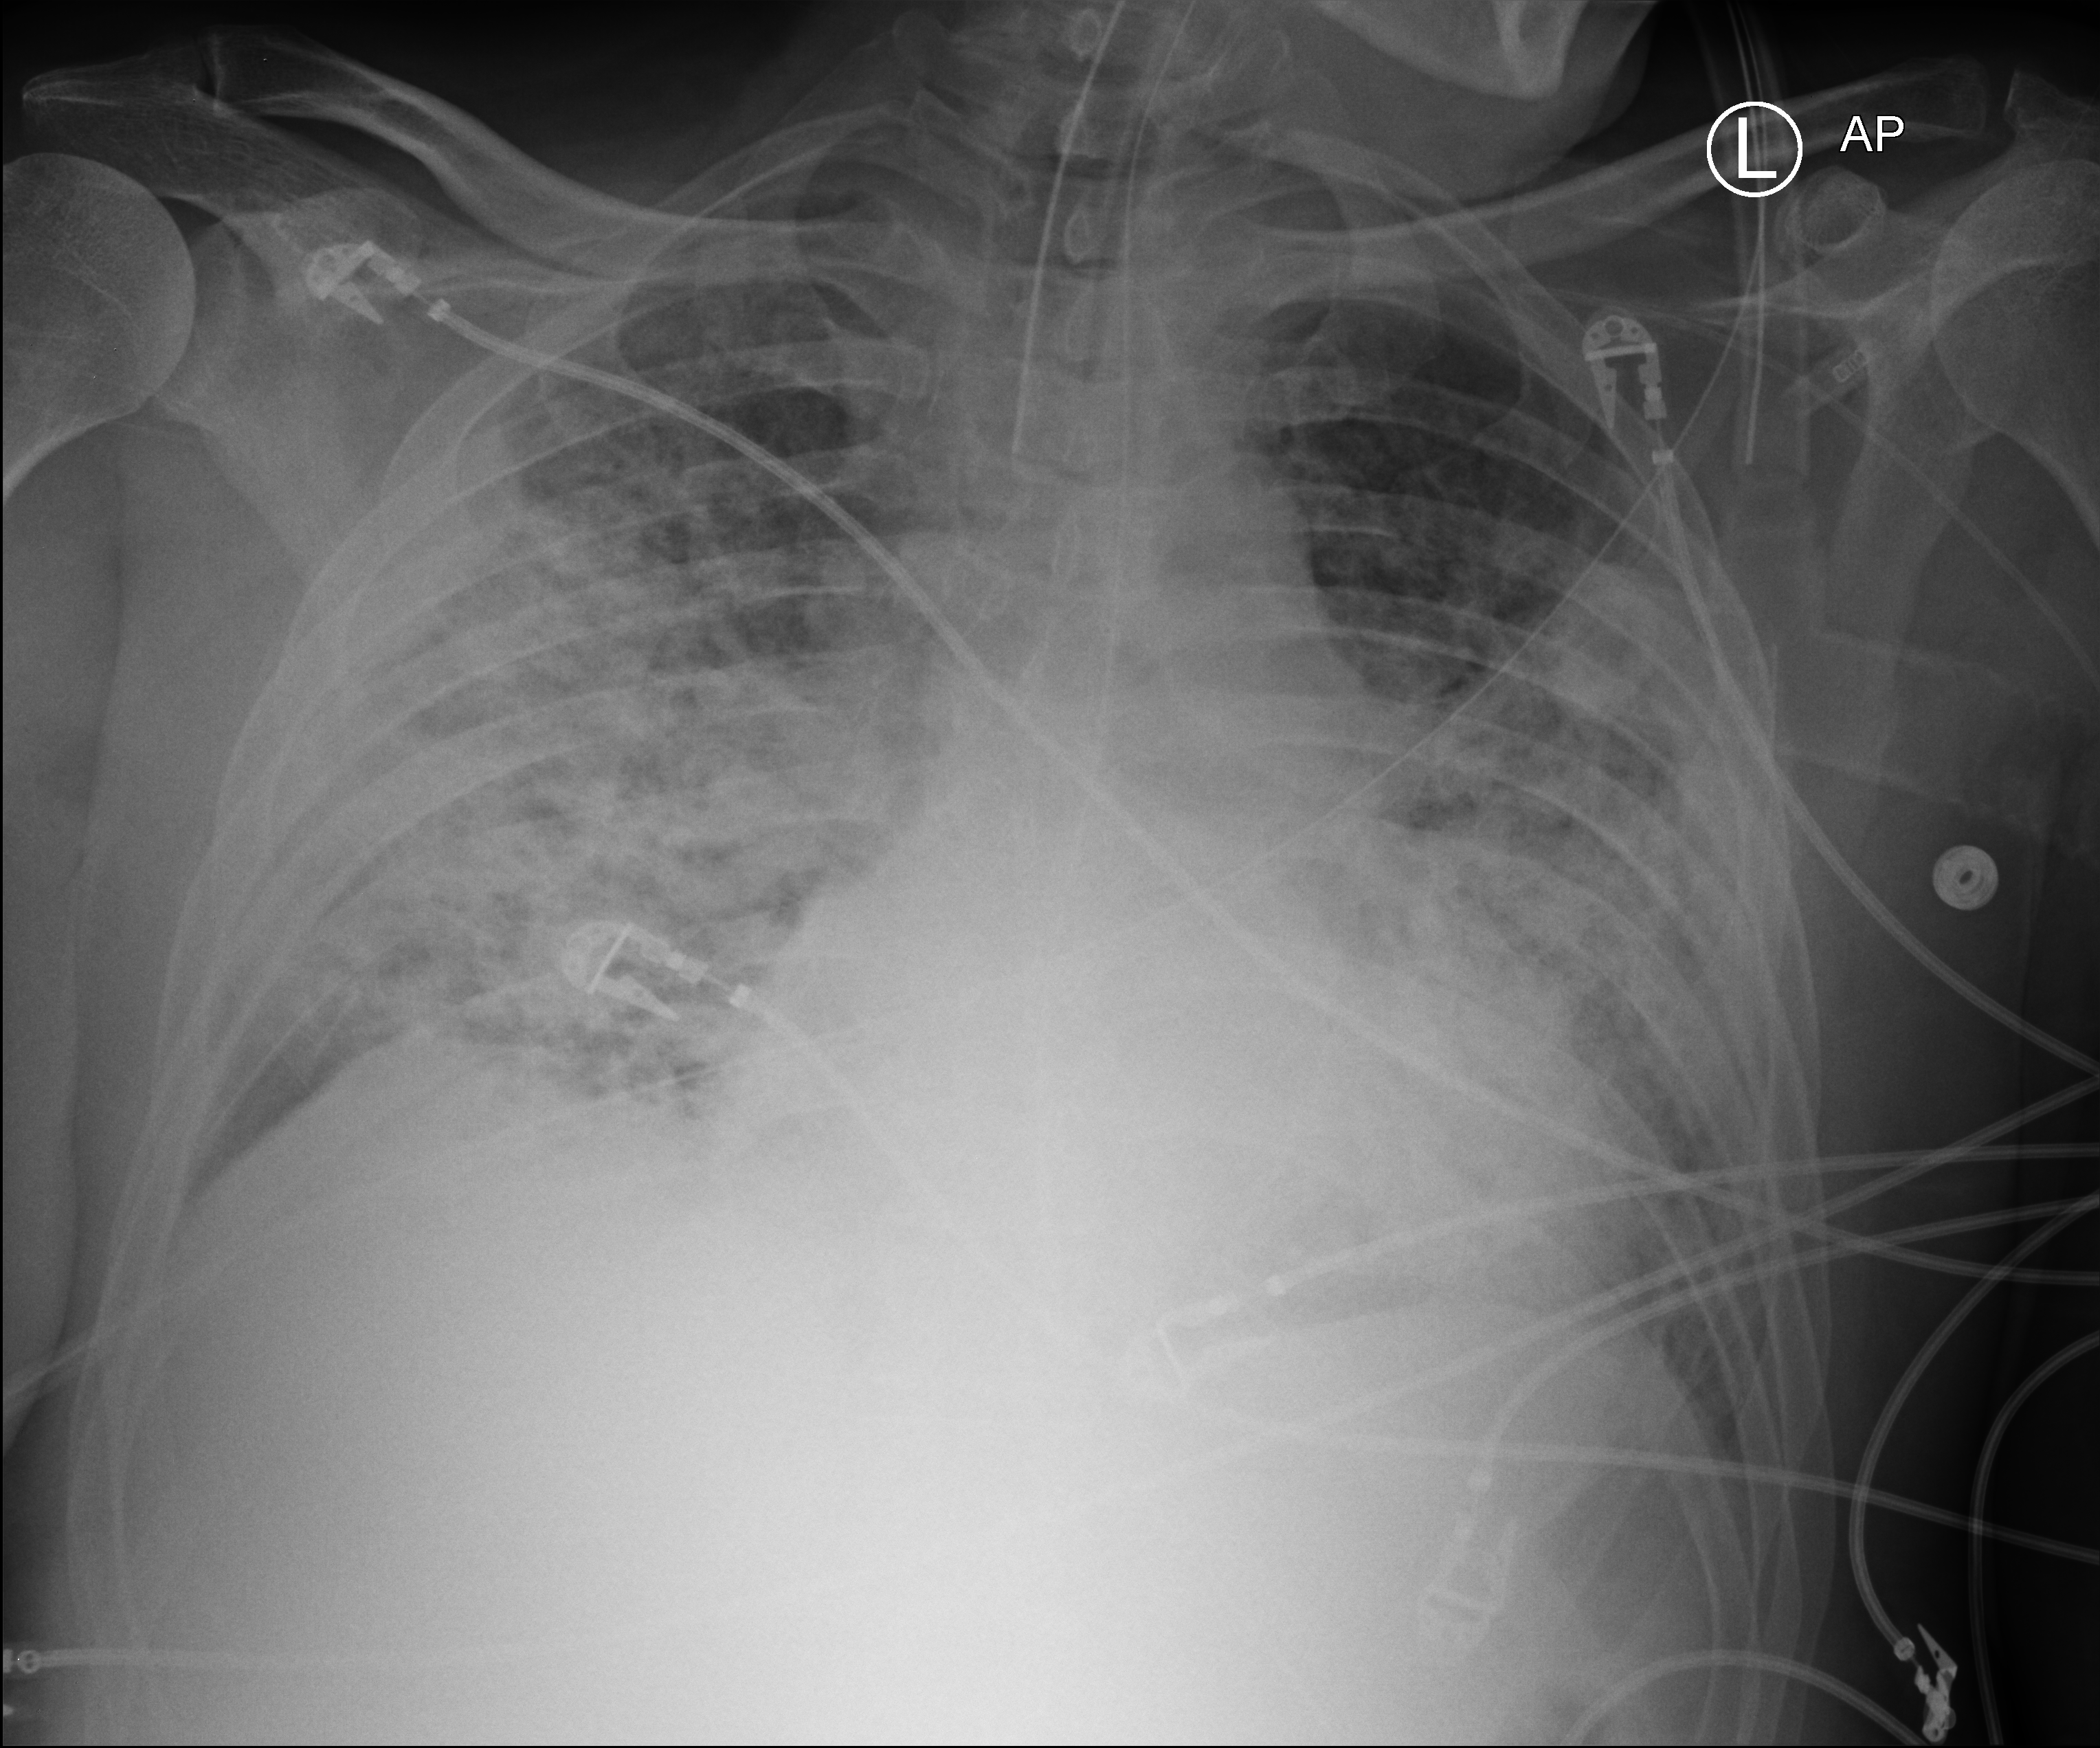
Chest X-ray (portable); anteroposterior (AP) projection. Patient hospitalised with COVID-19; male, aged 18–59 years.
Admission-level facts for this patient (not findings on this image; timing relative to this image not recorded):
- admitted to intensive care during this hospital stay: yes
- length of hospital stay: 75 days